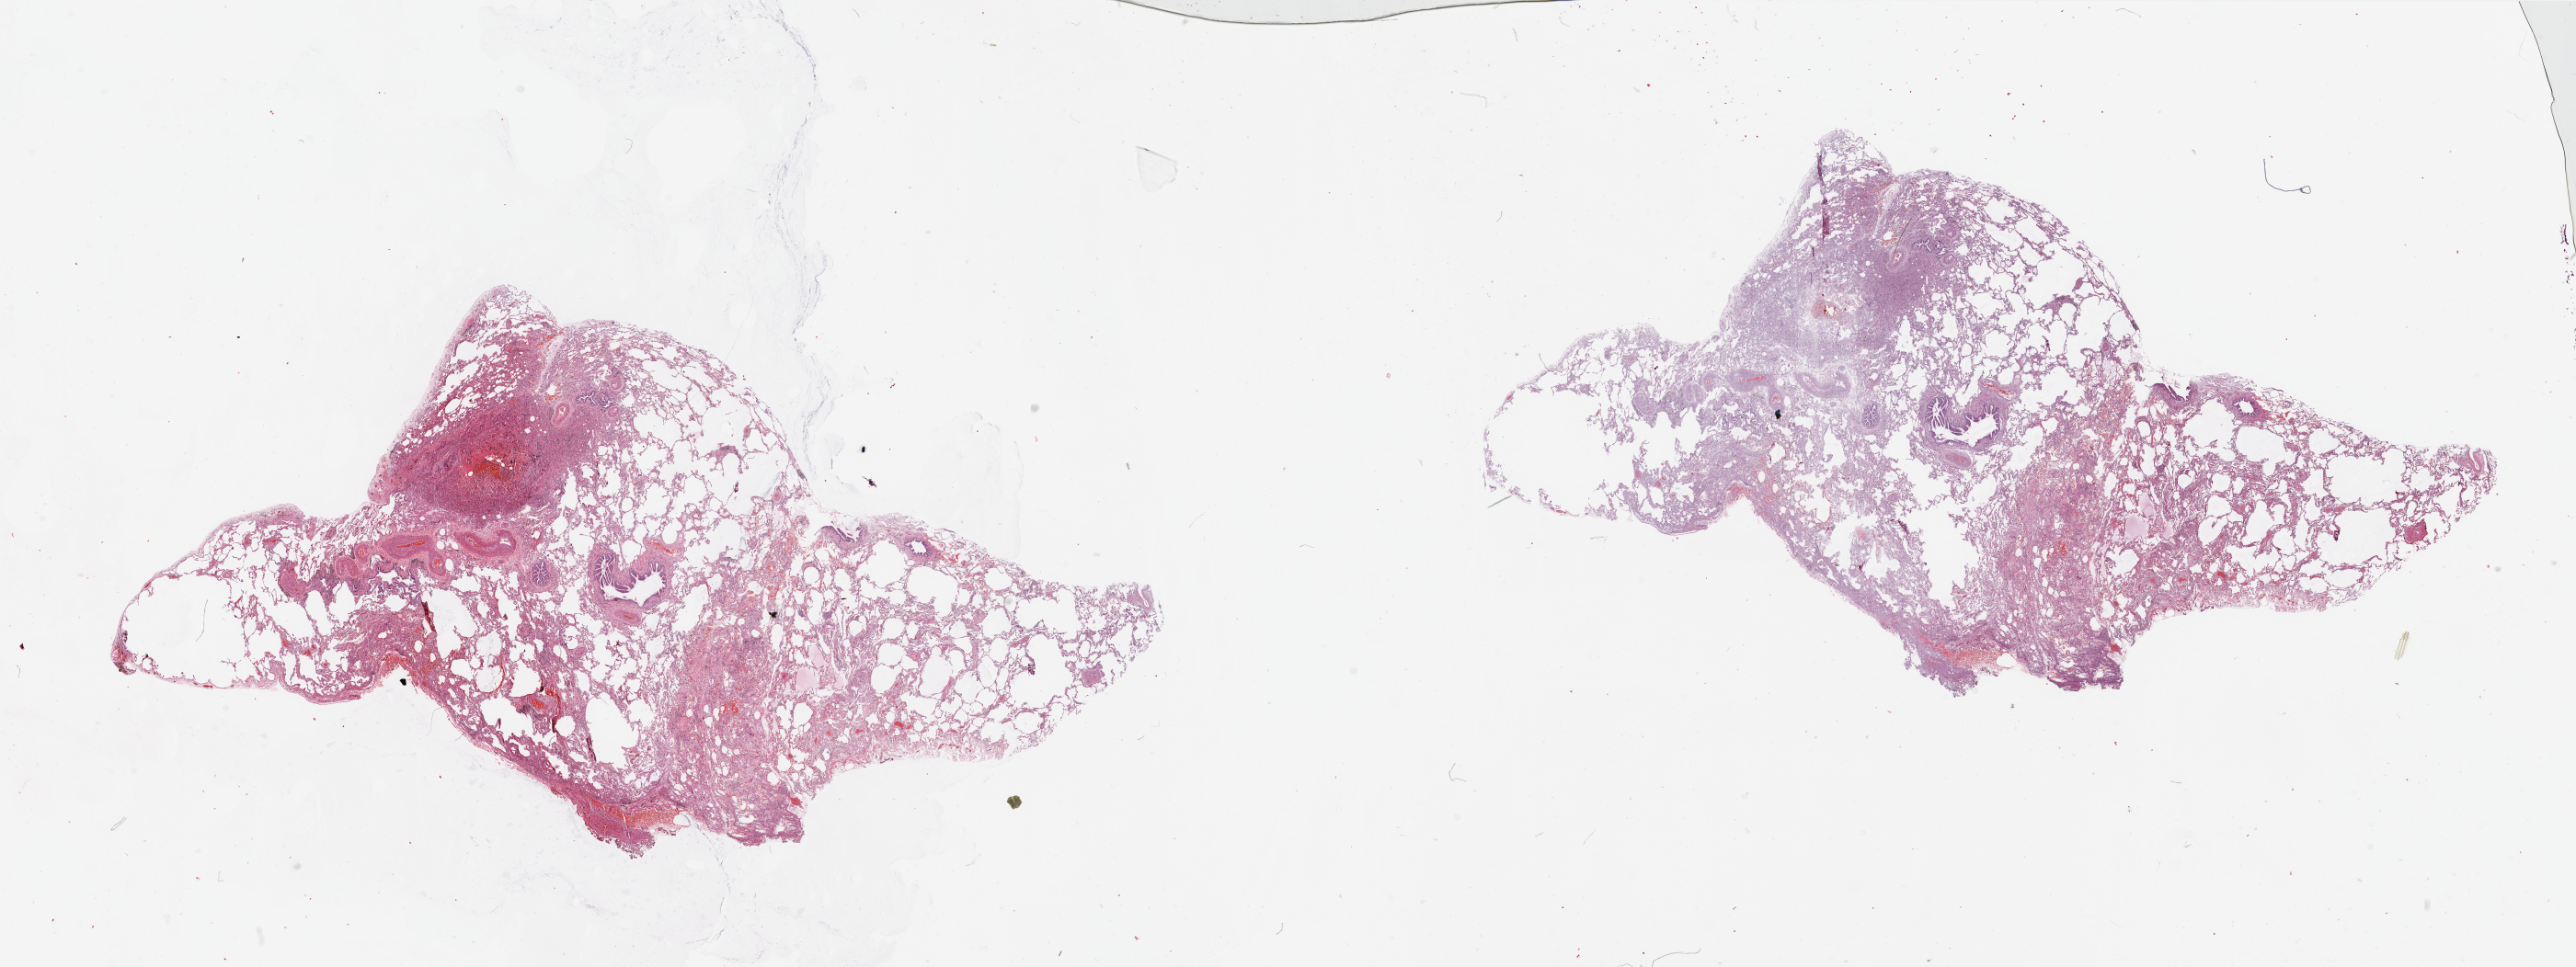
Hematoxylin and eosin (H&E) stained whole-slide image, whole scanned area (about 44.3 x 16.6 mm, from a 20x scan) shown as a low-resolution overview. Lung, normal (non-tumour) tissue. 65-year-old male patient.
This section: normal (non-tumour) tissue from the same patient. Patient diagnosis: Adenocarcinoma, NOS.